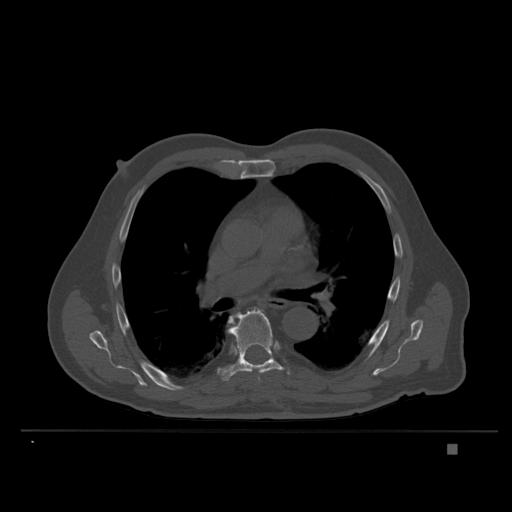
CT including the spine, one axial slice. Slice 246 of 435 in the series (ordered by position). Bone window (W 1800 / L 400 HU). 1.5 mm slice thickness. 512 × 512 image matrix, field of view 434 × 434 mm. Male patient, age 73 years. Case-level facts recorded for this patient, not image findings: primary cancer: skin.
Annotated regions visible in this slice (semi-automatically segmented with operator editing):
- T7 vertebra: box from (x=218, y=309) to (x=284, y=381) px